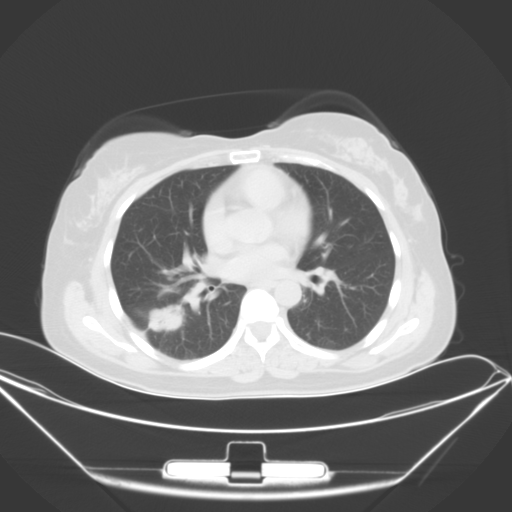
Chest CT, one axial slice. Slice 20 of 46 in the series (ordered by position). 120 kVp. Lung window (W 1500 / L -600 HU). 5 mm slice thickness. 512 × 512 image matrix, field of view 407 × 407 mm. Female patient, age 42 years. Case-level facts recorded for this patient, not image findings: clinical TNM (as recorded): T1c N0 M1a.
Structures marked on this image (bounding box drawn by a radiologist):
- lung tumour (recorded histology: adenocarcinoma): box from (x=144, y=301) to (x=188, y=339) px